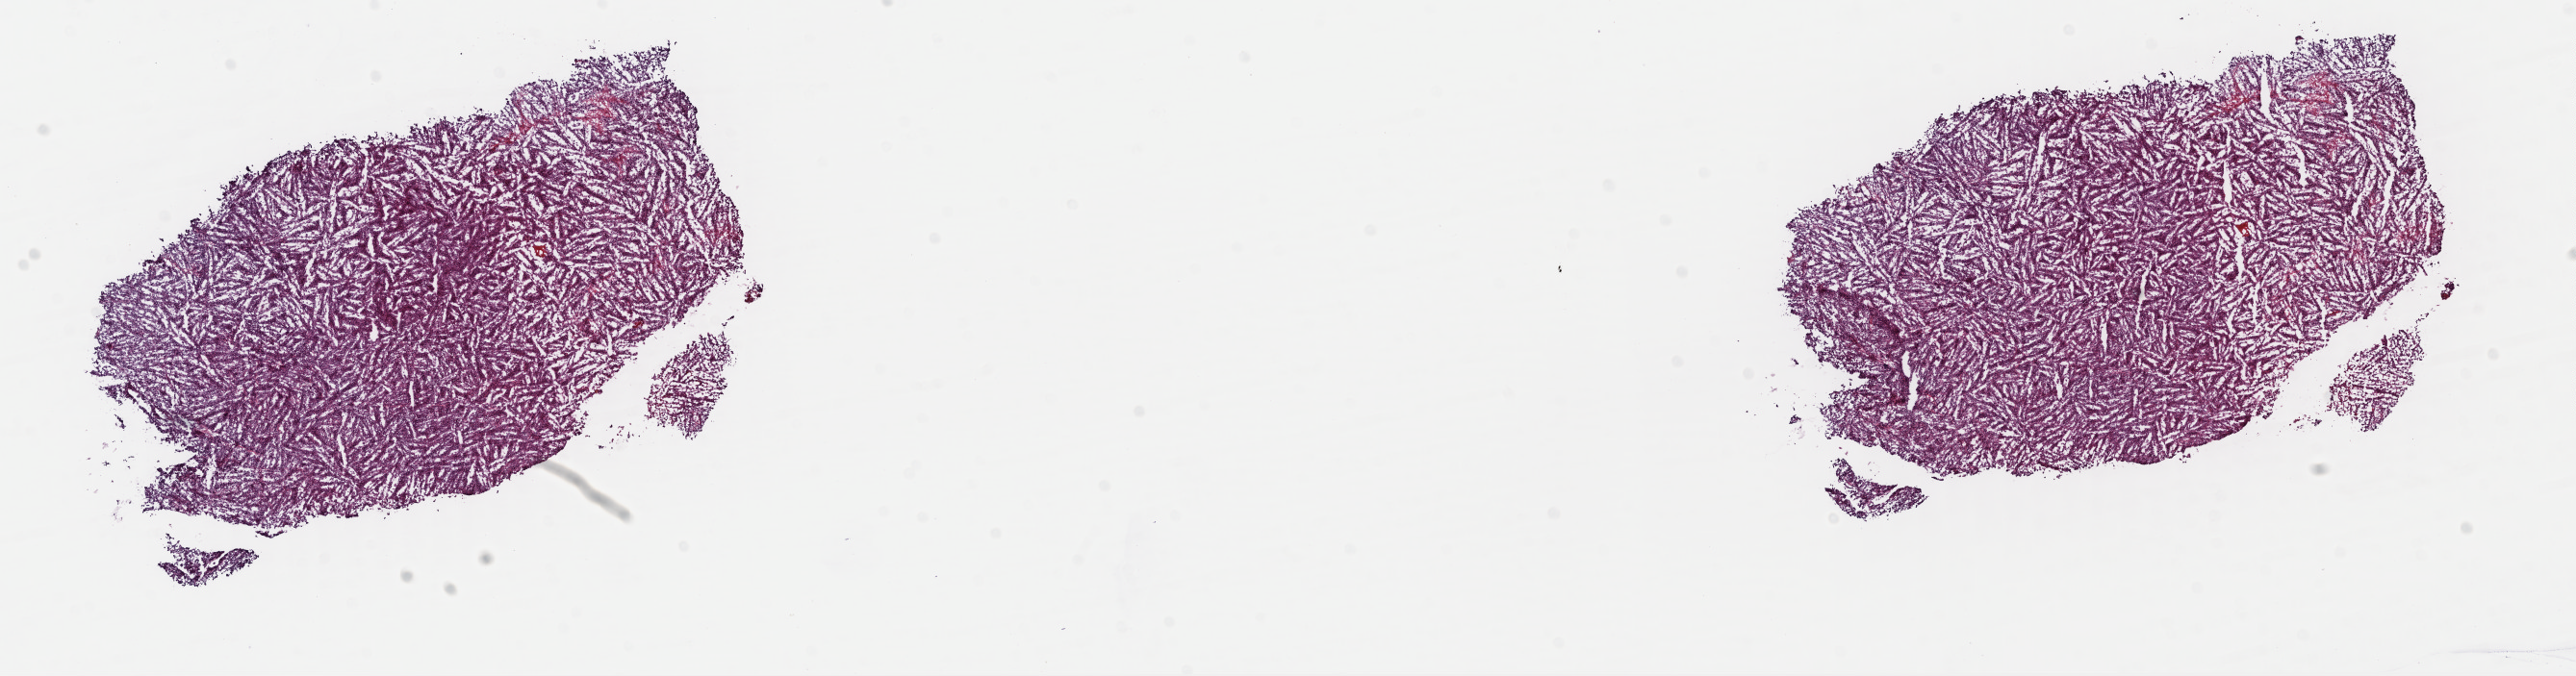
Digitized H&E-stained tissue section (whole slide) — whole scanned area (about 21.0 x 5.5 mm, from a 40x scan) shown as a low-resolution overview; frozen section; bladder, primary tumour sample. Male, age 75 years at initial diagnosis. Histologic grade: high grade. Pathologist review of this section (percent, as recorded): tumour cells 85%, tumour nuclei 90%, normal cells 0%, stromal cells 10%, necrosis 5%. Inflammatory infiltration, as recorded: lymphocyte infiltration 2%, monocyte infiltration 0%, neutrophil infiltration 0%.
AJCC pathologic stage: II (7th edition). Lymph nodes positive (case pathology): 0 of 12 examined. Histologic diagnosis: Papillary transitional cell carcinoma (posterior wall of bladder).